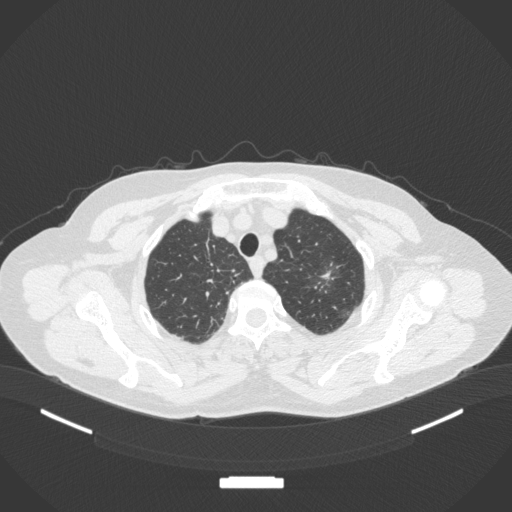
Chest CT, one axial slice; position 309 of 369 along the scan axis; 120 kVp; lung window (W 1500 / L -600 HU); 1 mm slice thickness; 512 × 512 image matrix, field of view 400 × 400 mm. Patient: female, 64 years. Case-level facts recorded for this patient, not image findings: clinical TNM (as recorded): T1c N0 M0; histopathological grade: G1.
Outlined on this slice (rectangle marked by the reading radiologist):
- lung tumour (recorded histology: adenocarcinoma): bounding box [x1, y1, x2, y2] px = [306, 248, 346, 300]